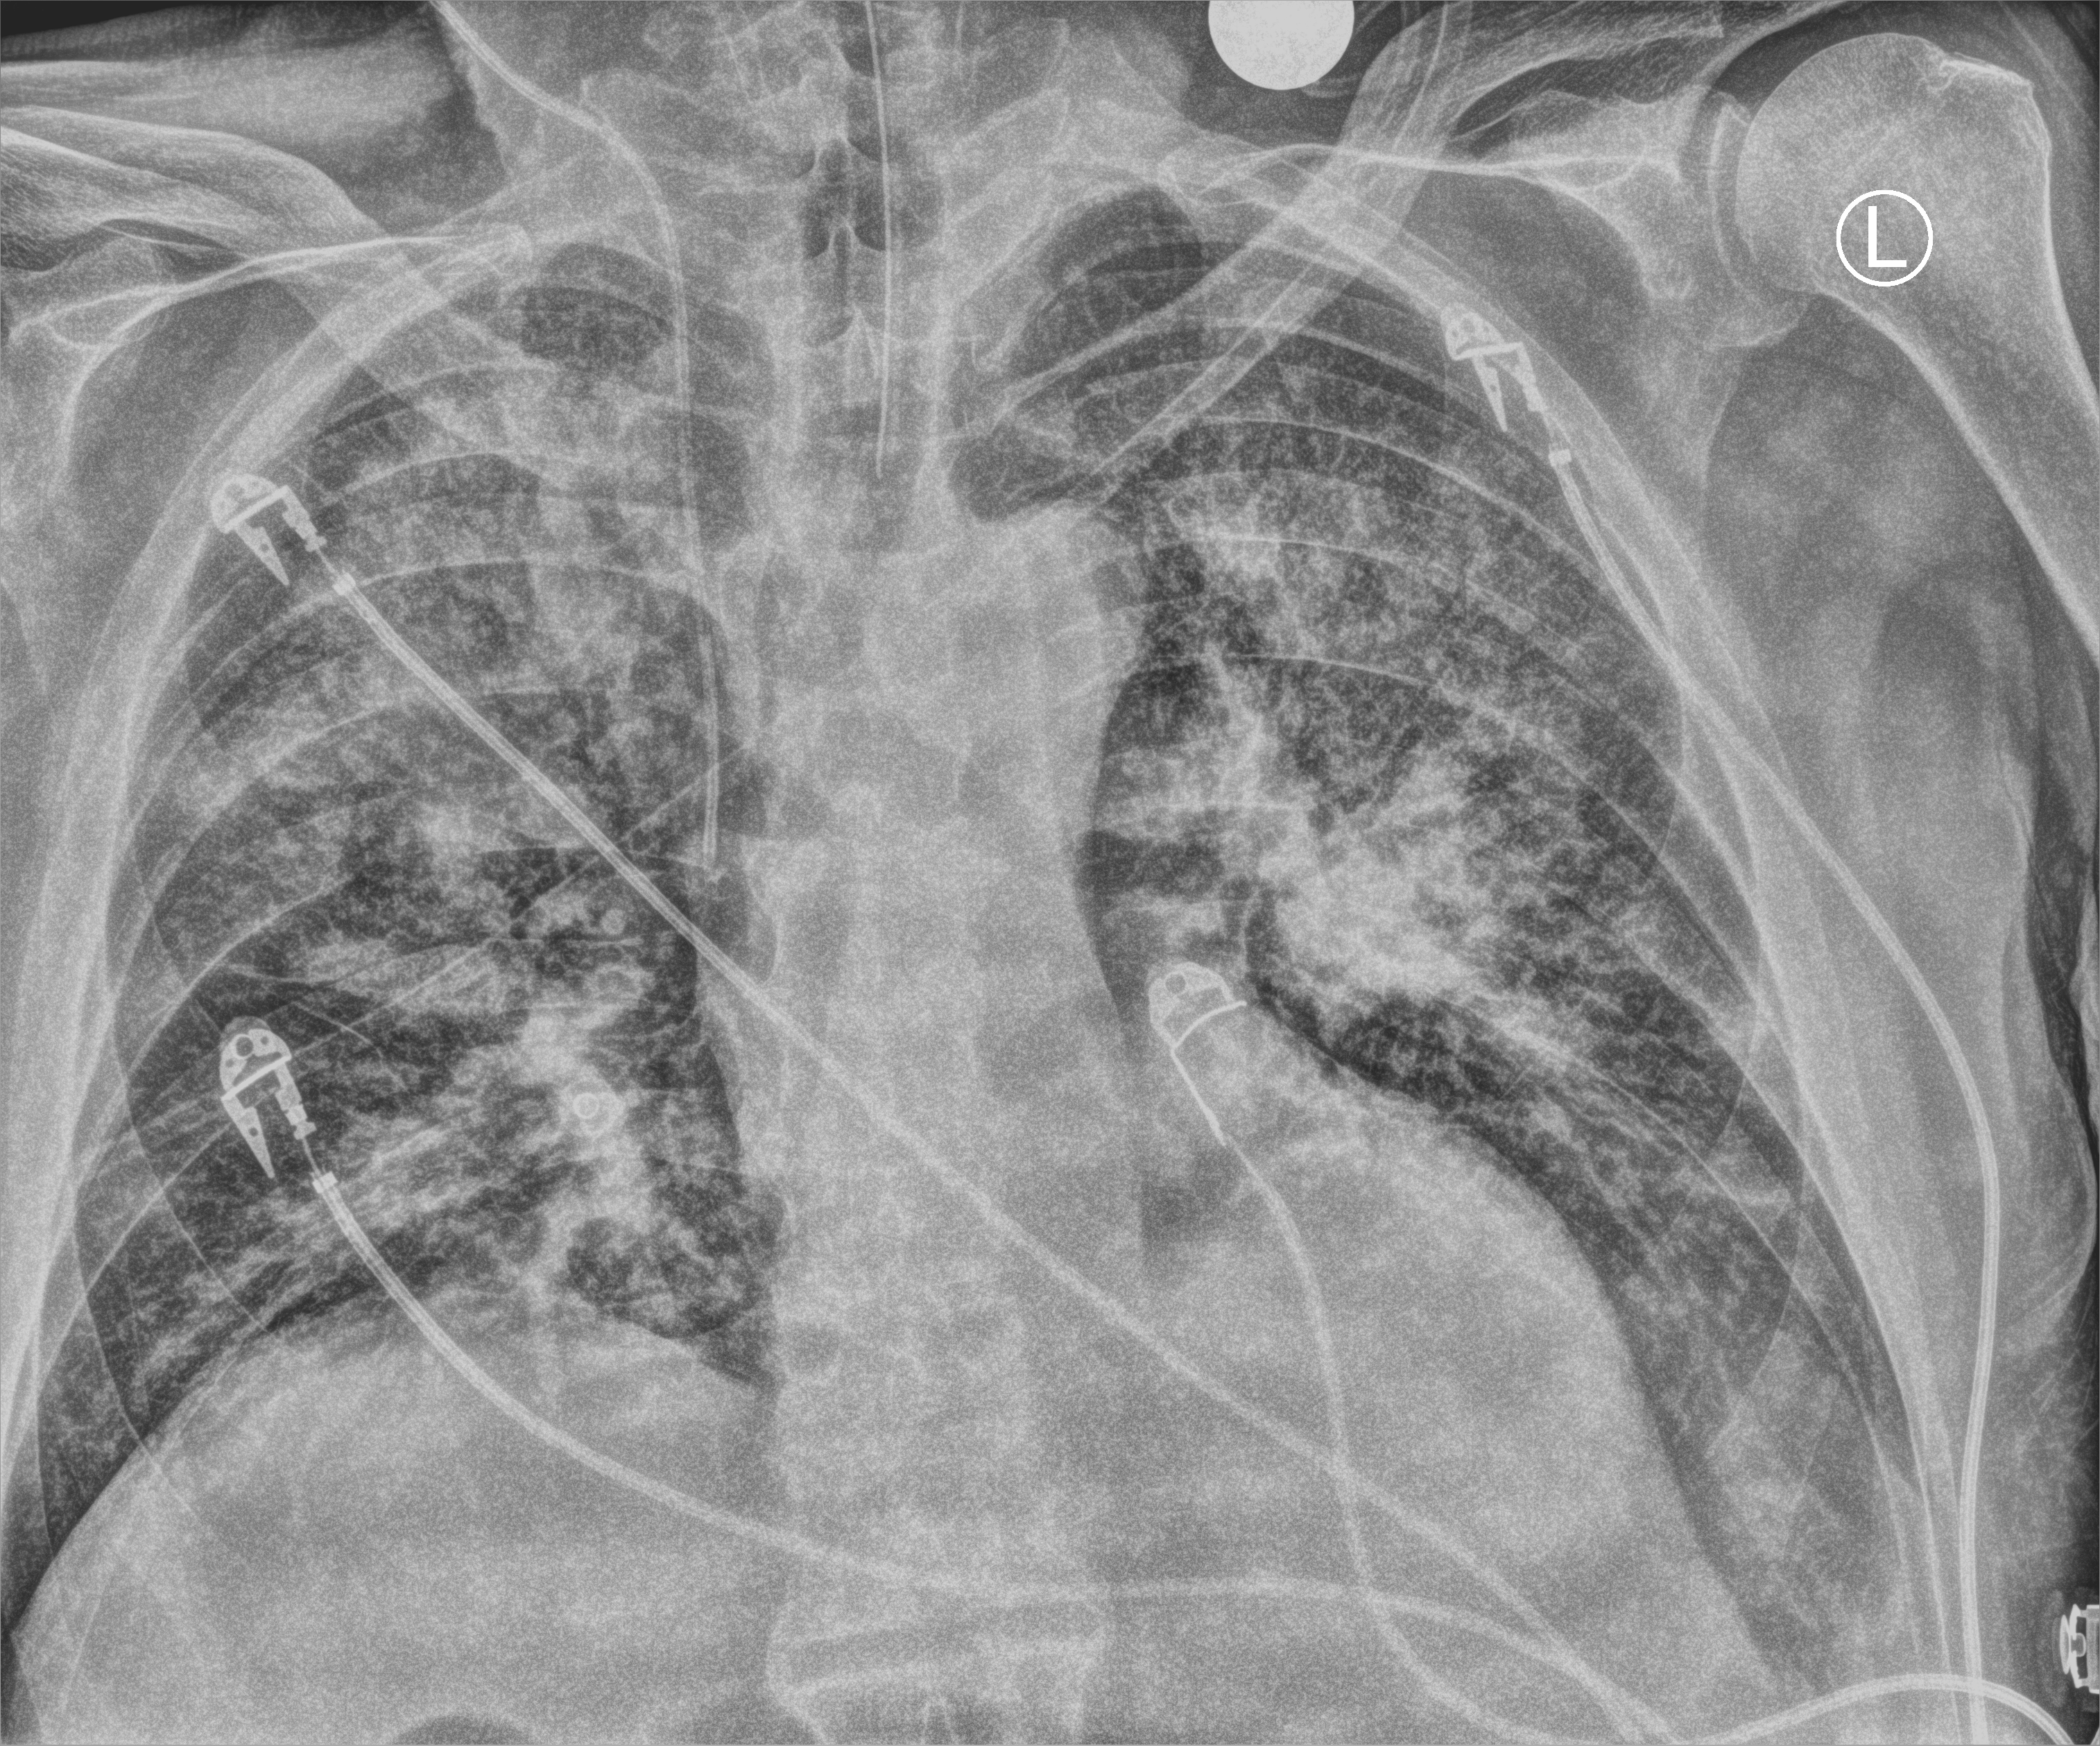
Portable chest radiograph; anteroposterior (AP) projection. Male patient hospitalised with COVID-19, age 75–90 years.
From the hospital-stay record, not from the radiograph (when in the stay this image was taken is not recorded): mechanically ventilated during this hospital stay: yes.